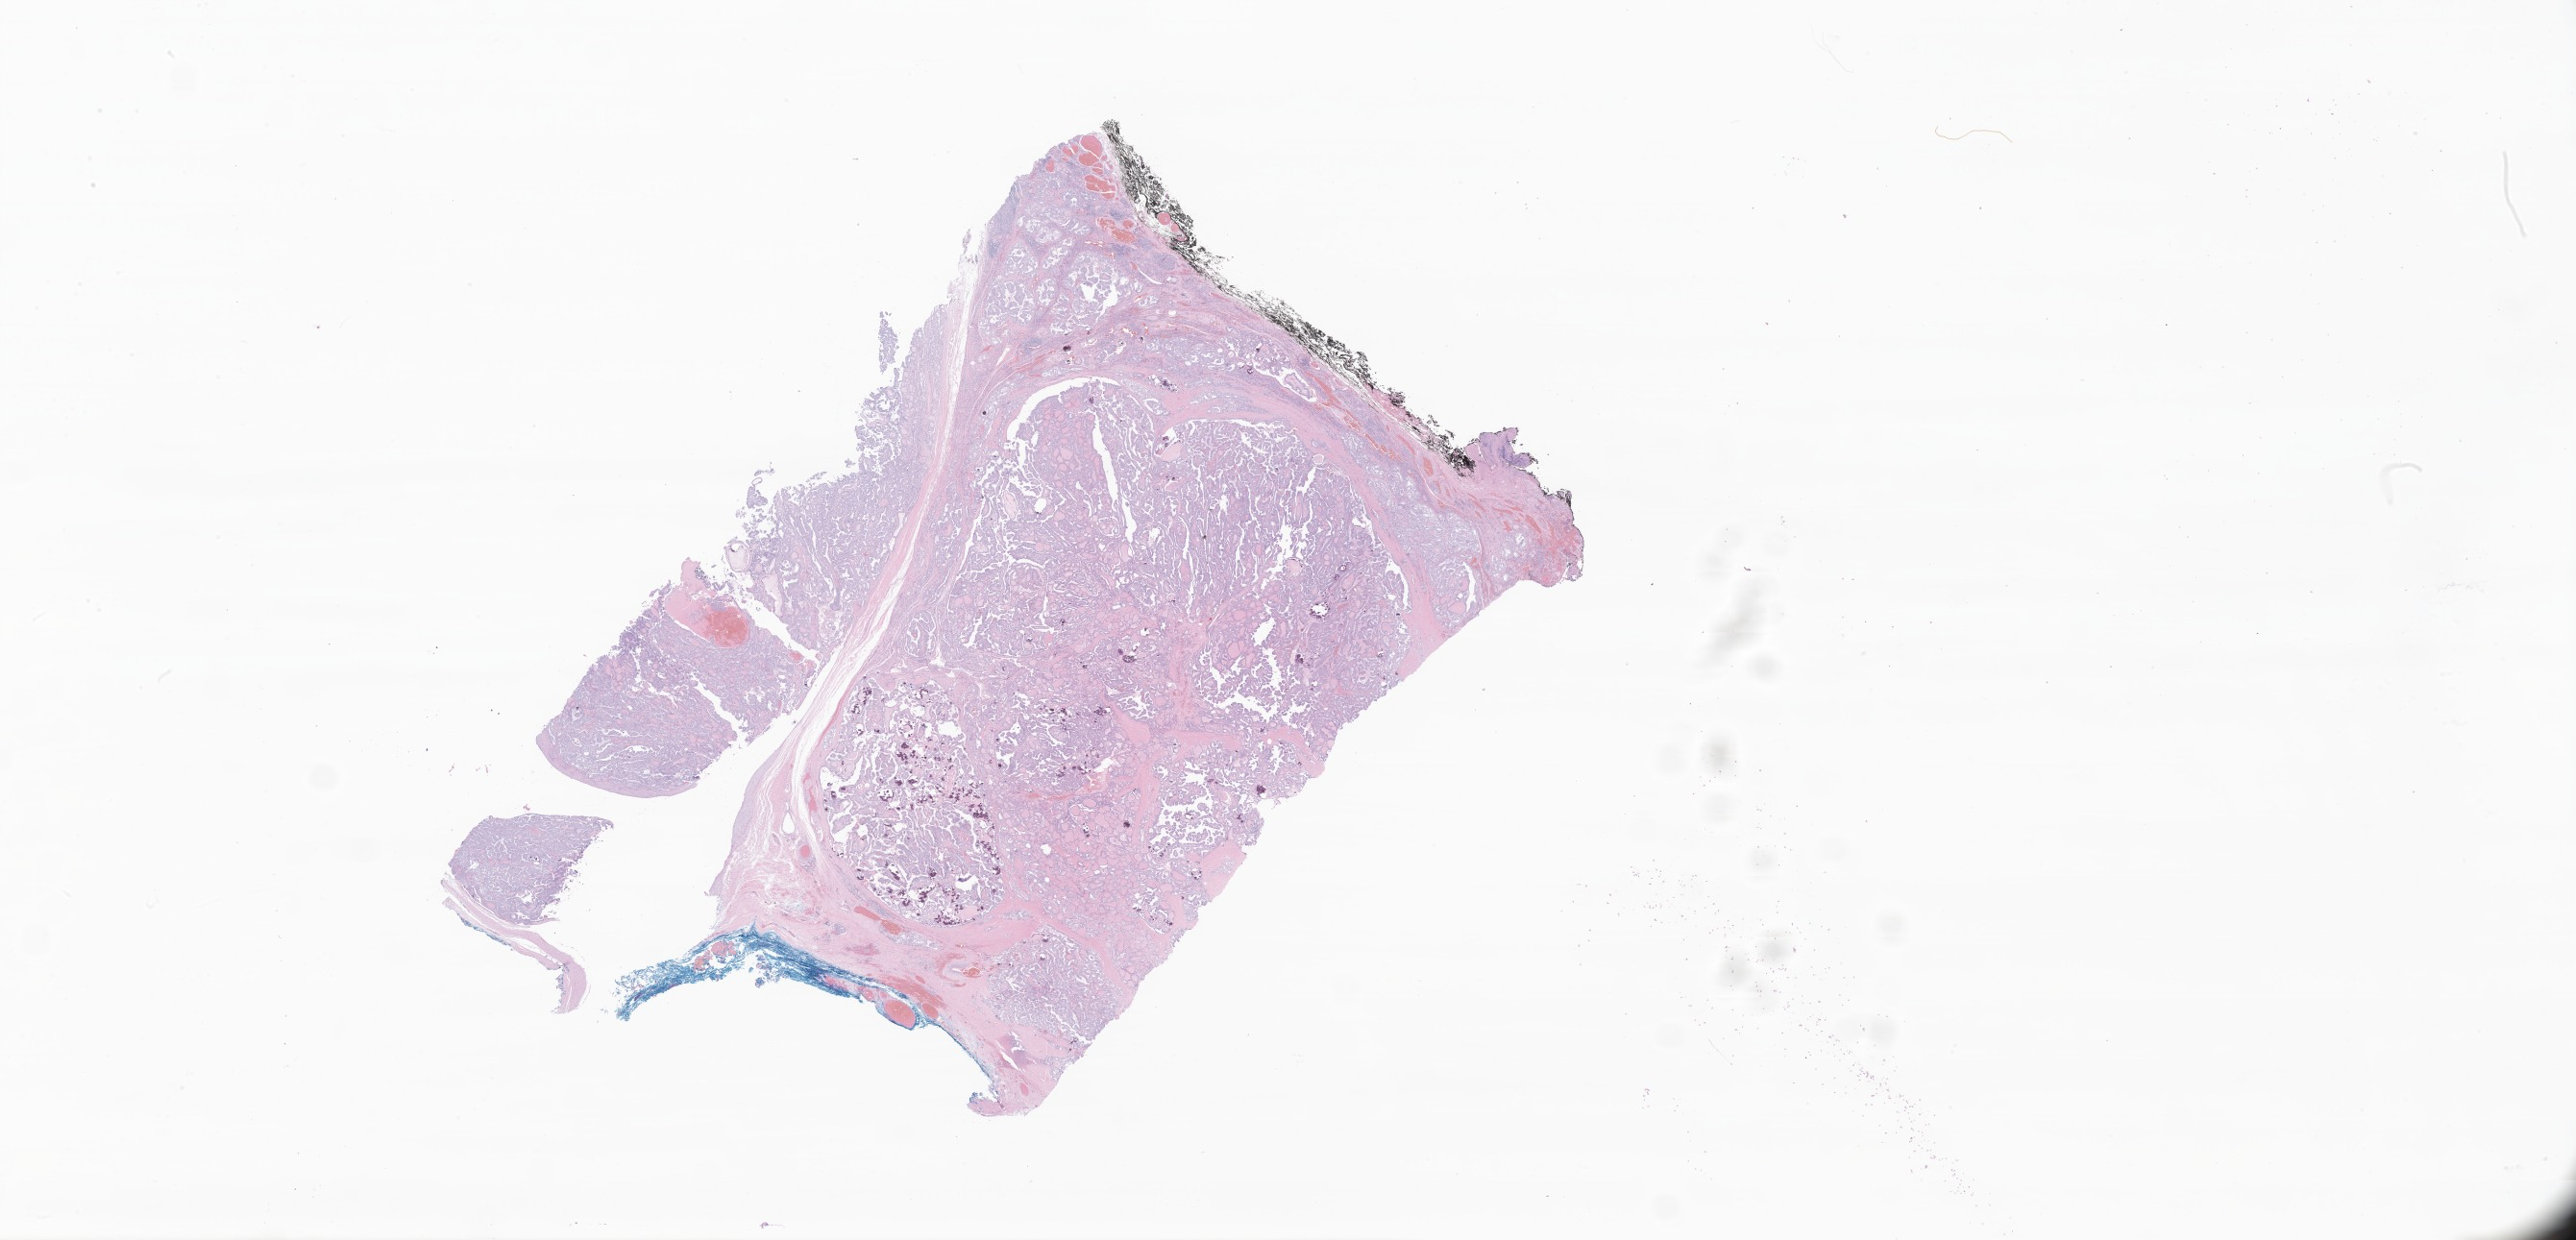
Whole-slide image, H&E stain of tumor tissue from the thyroid, whole scanned area (about 45.2 x 21.8 mm) shown as a low-resolution overview. Formalin-fixed paraffin-embedded section. Patient female; age 213 months (17 years 9 months).
Diagnosis (ICD-O-3 morphology term): Papillary carcinoma, NOS.